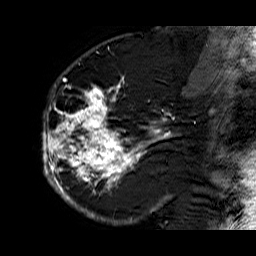
Breast MRI (dynamic contrast-enhanced), one sagittal slice; slice 38 of 60 in the series (ordered by position); dynamic contrast-enhanced series, time point 2 of 6 at this slice position (early post-contrast); 1.5 T; TE 6.3 ms, TR 32.9 ms; 4 mm slice thickness; 256 × 256 image matrix, field of view 200 × 200 mm. Female patient. Case-level facts recorded for this patient, not image findings: setting: breast cancer imaged before/during neoadjuvant chemotherapy; receptor status: HR-positive, HER2-negative.
Outlined on this slice (semi-automatic segmentation, software-assisted and operator-edited):
- analysis volume of interest (the breast-tissue region the enhancement analysis was run in; not a lesion): bounding box <41,74,176,210> (left, top, right, bottom; pixels)
- tumour enhancement mask (voxels above the 100 % enhancement threshold inside the analysis volume of interest): <42,74,174,210>